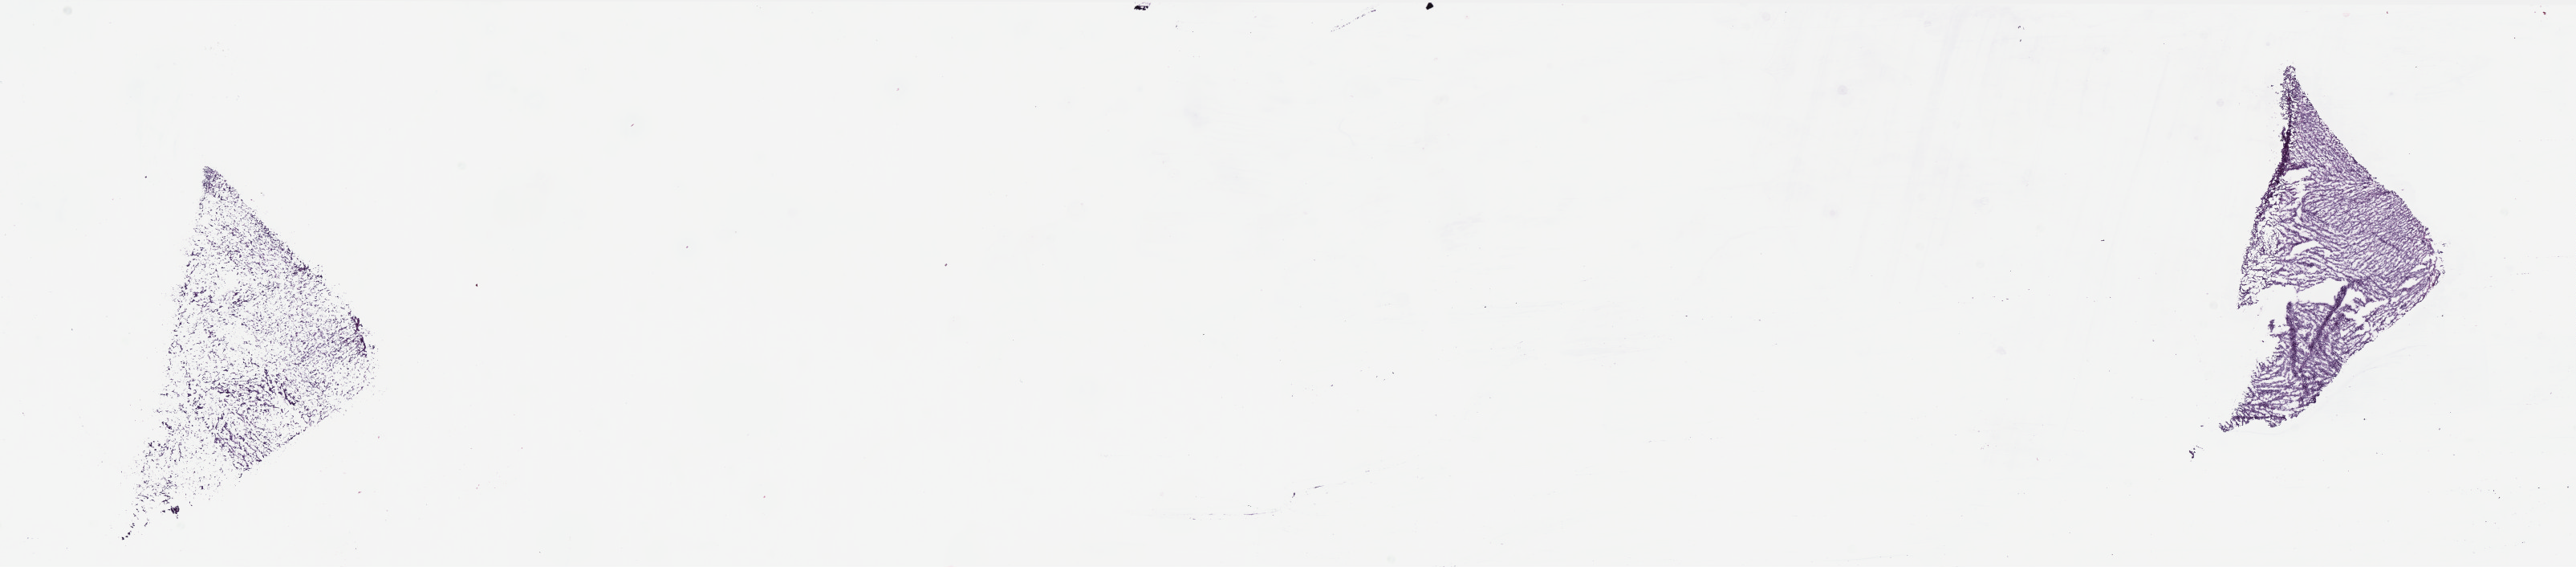
Whole-slide histology image, H&E, shown as a low-resolution overview of the whole scanned area (about 25.7 x 5.7 mm, acquisition: 40x scan). Frozen section. Primary tumour sample from the uterus. Female, age 69 years at initial diagnosis. Histologic grade: G3 (poorly differentiated). Pathologist review of this section (percent, as recorded): tumour cells 98%, tumour nuclei 60%, normal cells 0%, stromal cells 1%, necrosis 1%. Infiltration values recorded for this section: lymphocyte infiltration 25%, monocyte infiltration 0%, neutrophil infiltration 2%.
Diagnosis: Endometrioid adenocarcinoma, NOS. Lymph nodes positive (case pathology): 0 of 13 examined. FIGO stage: IA.